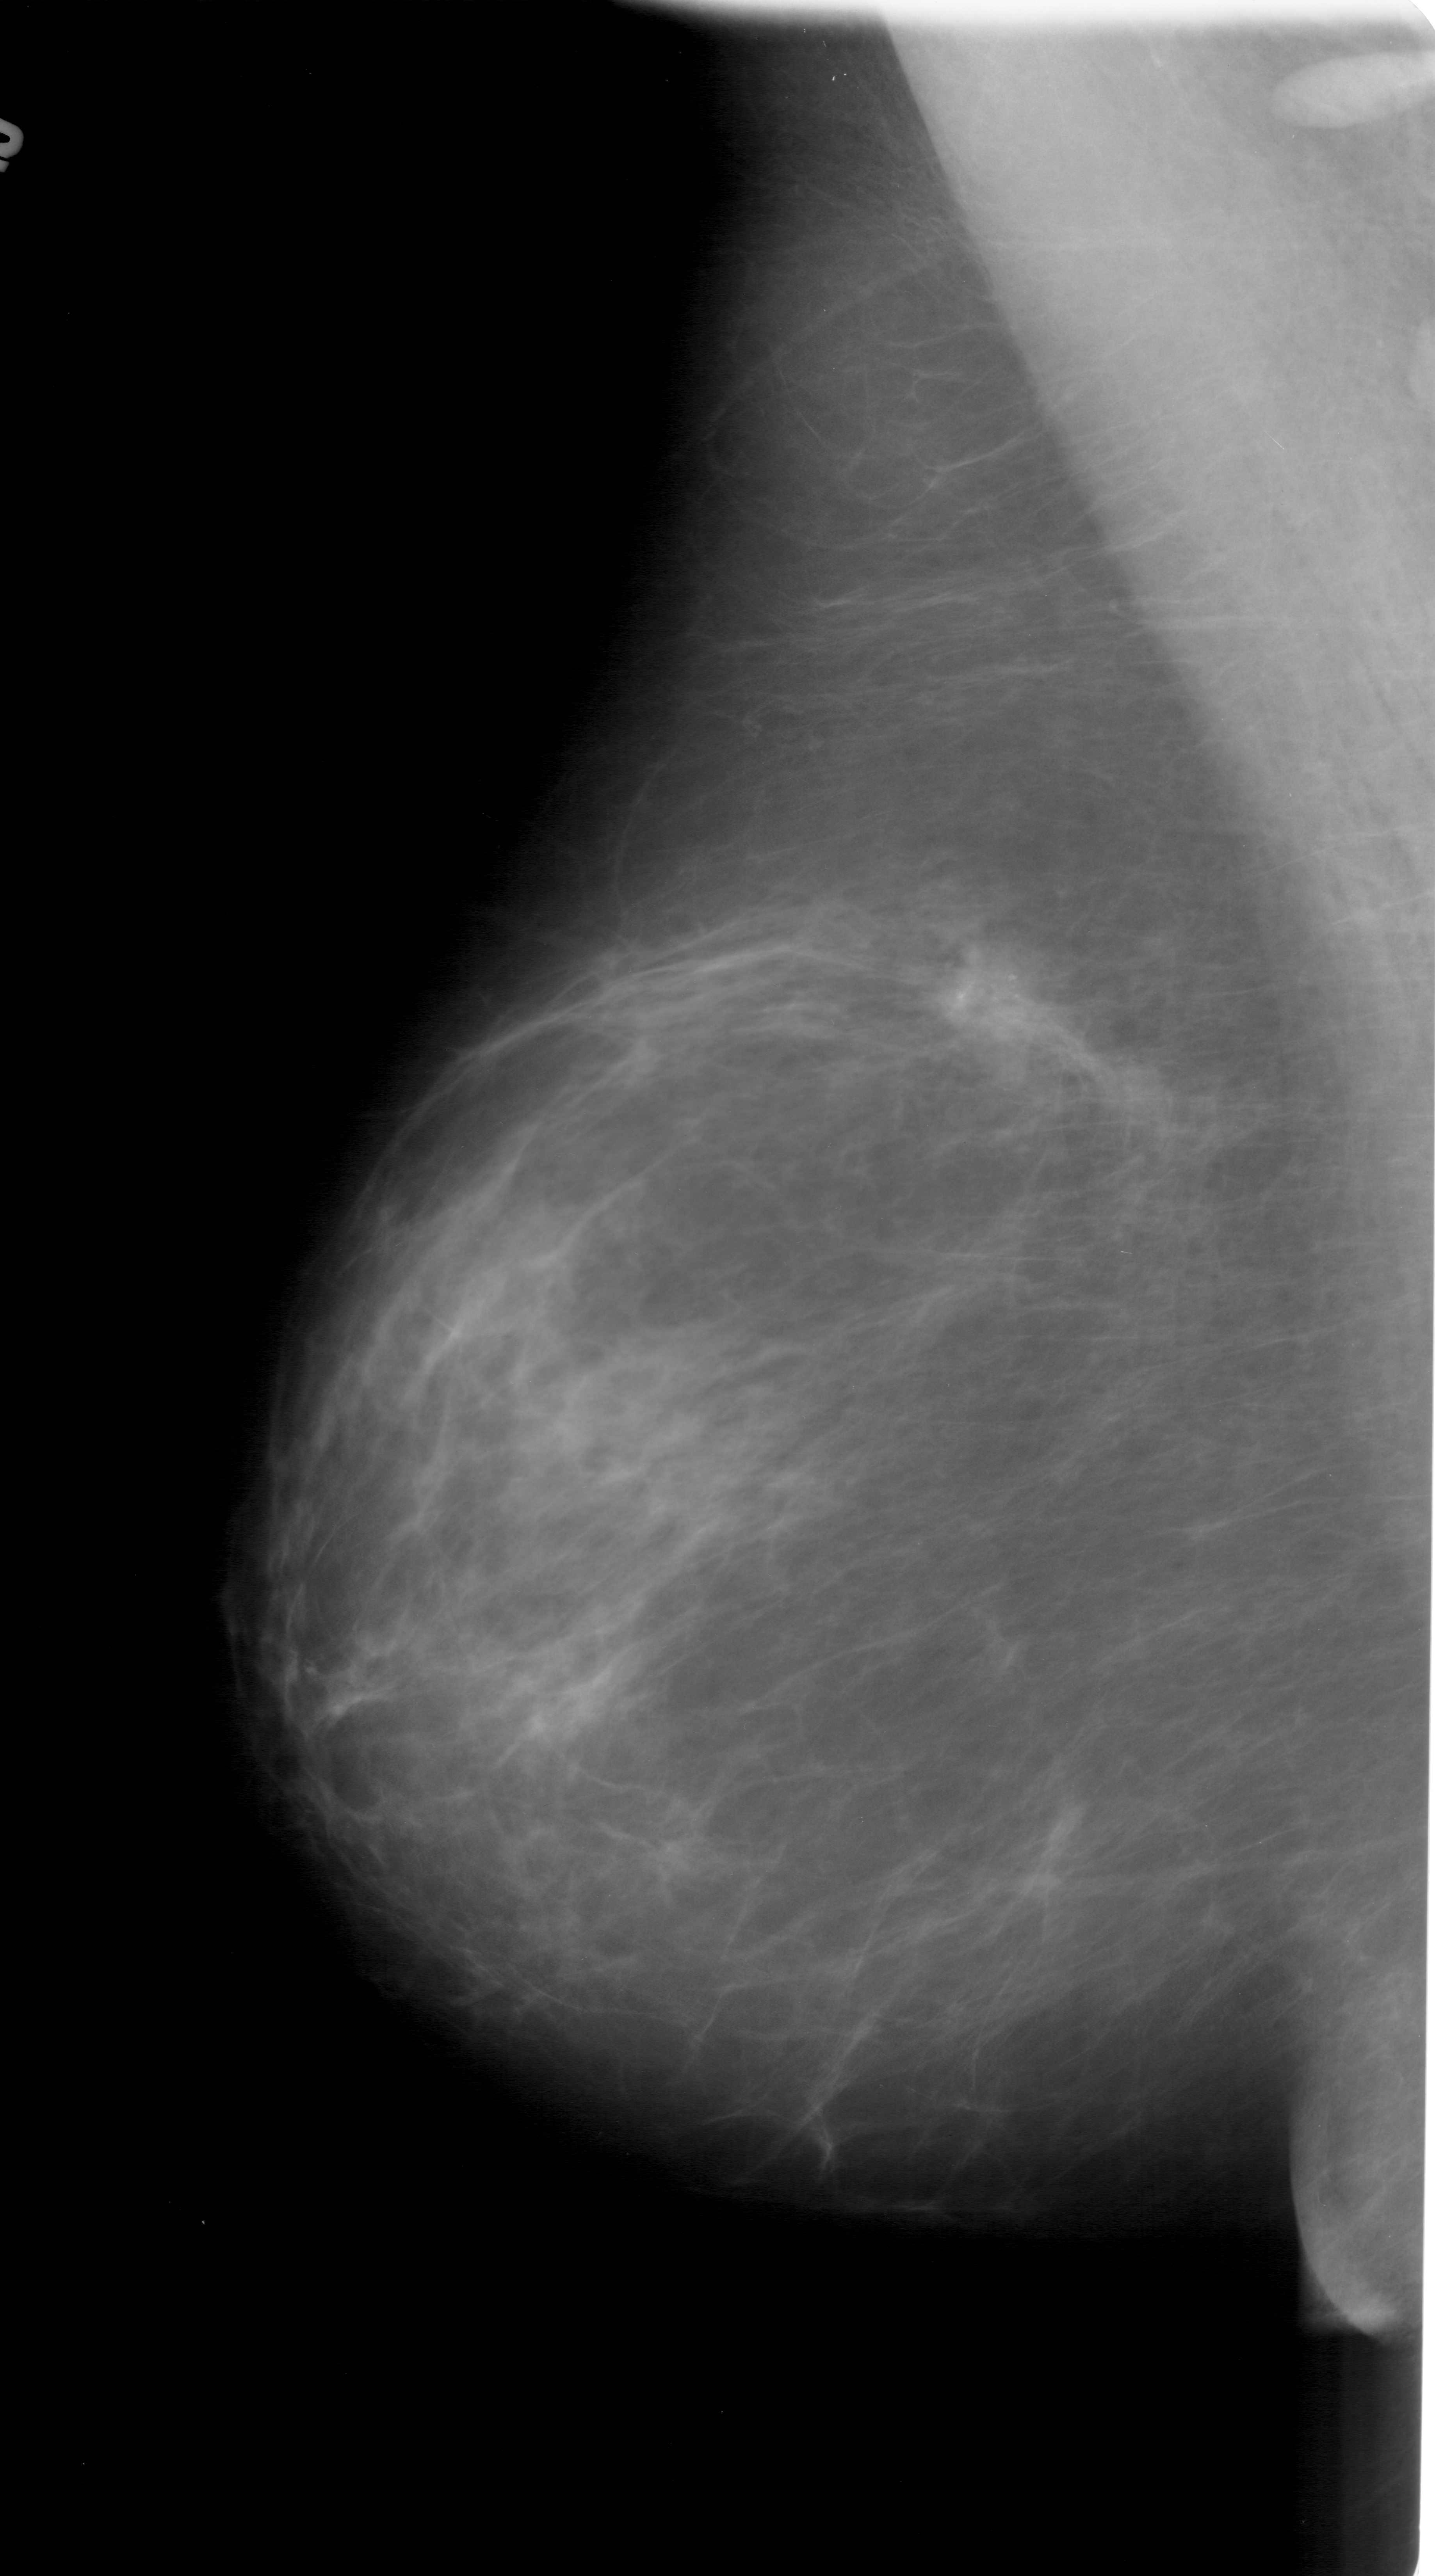
Scanned film-screen mammogram; left breast; mediolateral oblique (MLO) view; BI-RADS breast density category 2 (scale 1–4).
- Mass, shape asymmetric breast tissue, margins ill defined; BI-RADS assessment category 4; subtlety rating 4 on a 1 (subtle) to 5 (obvious) scale; pathology result (as recorded, not read from the image): malignant.